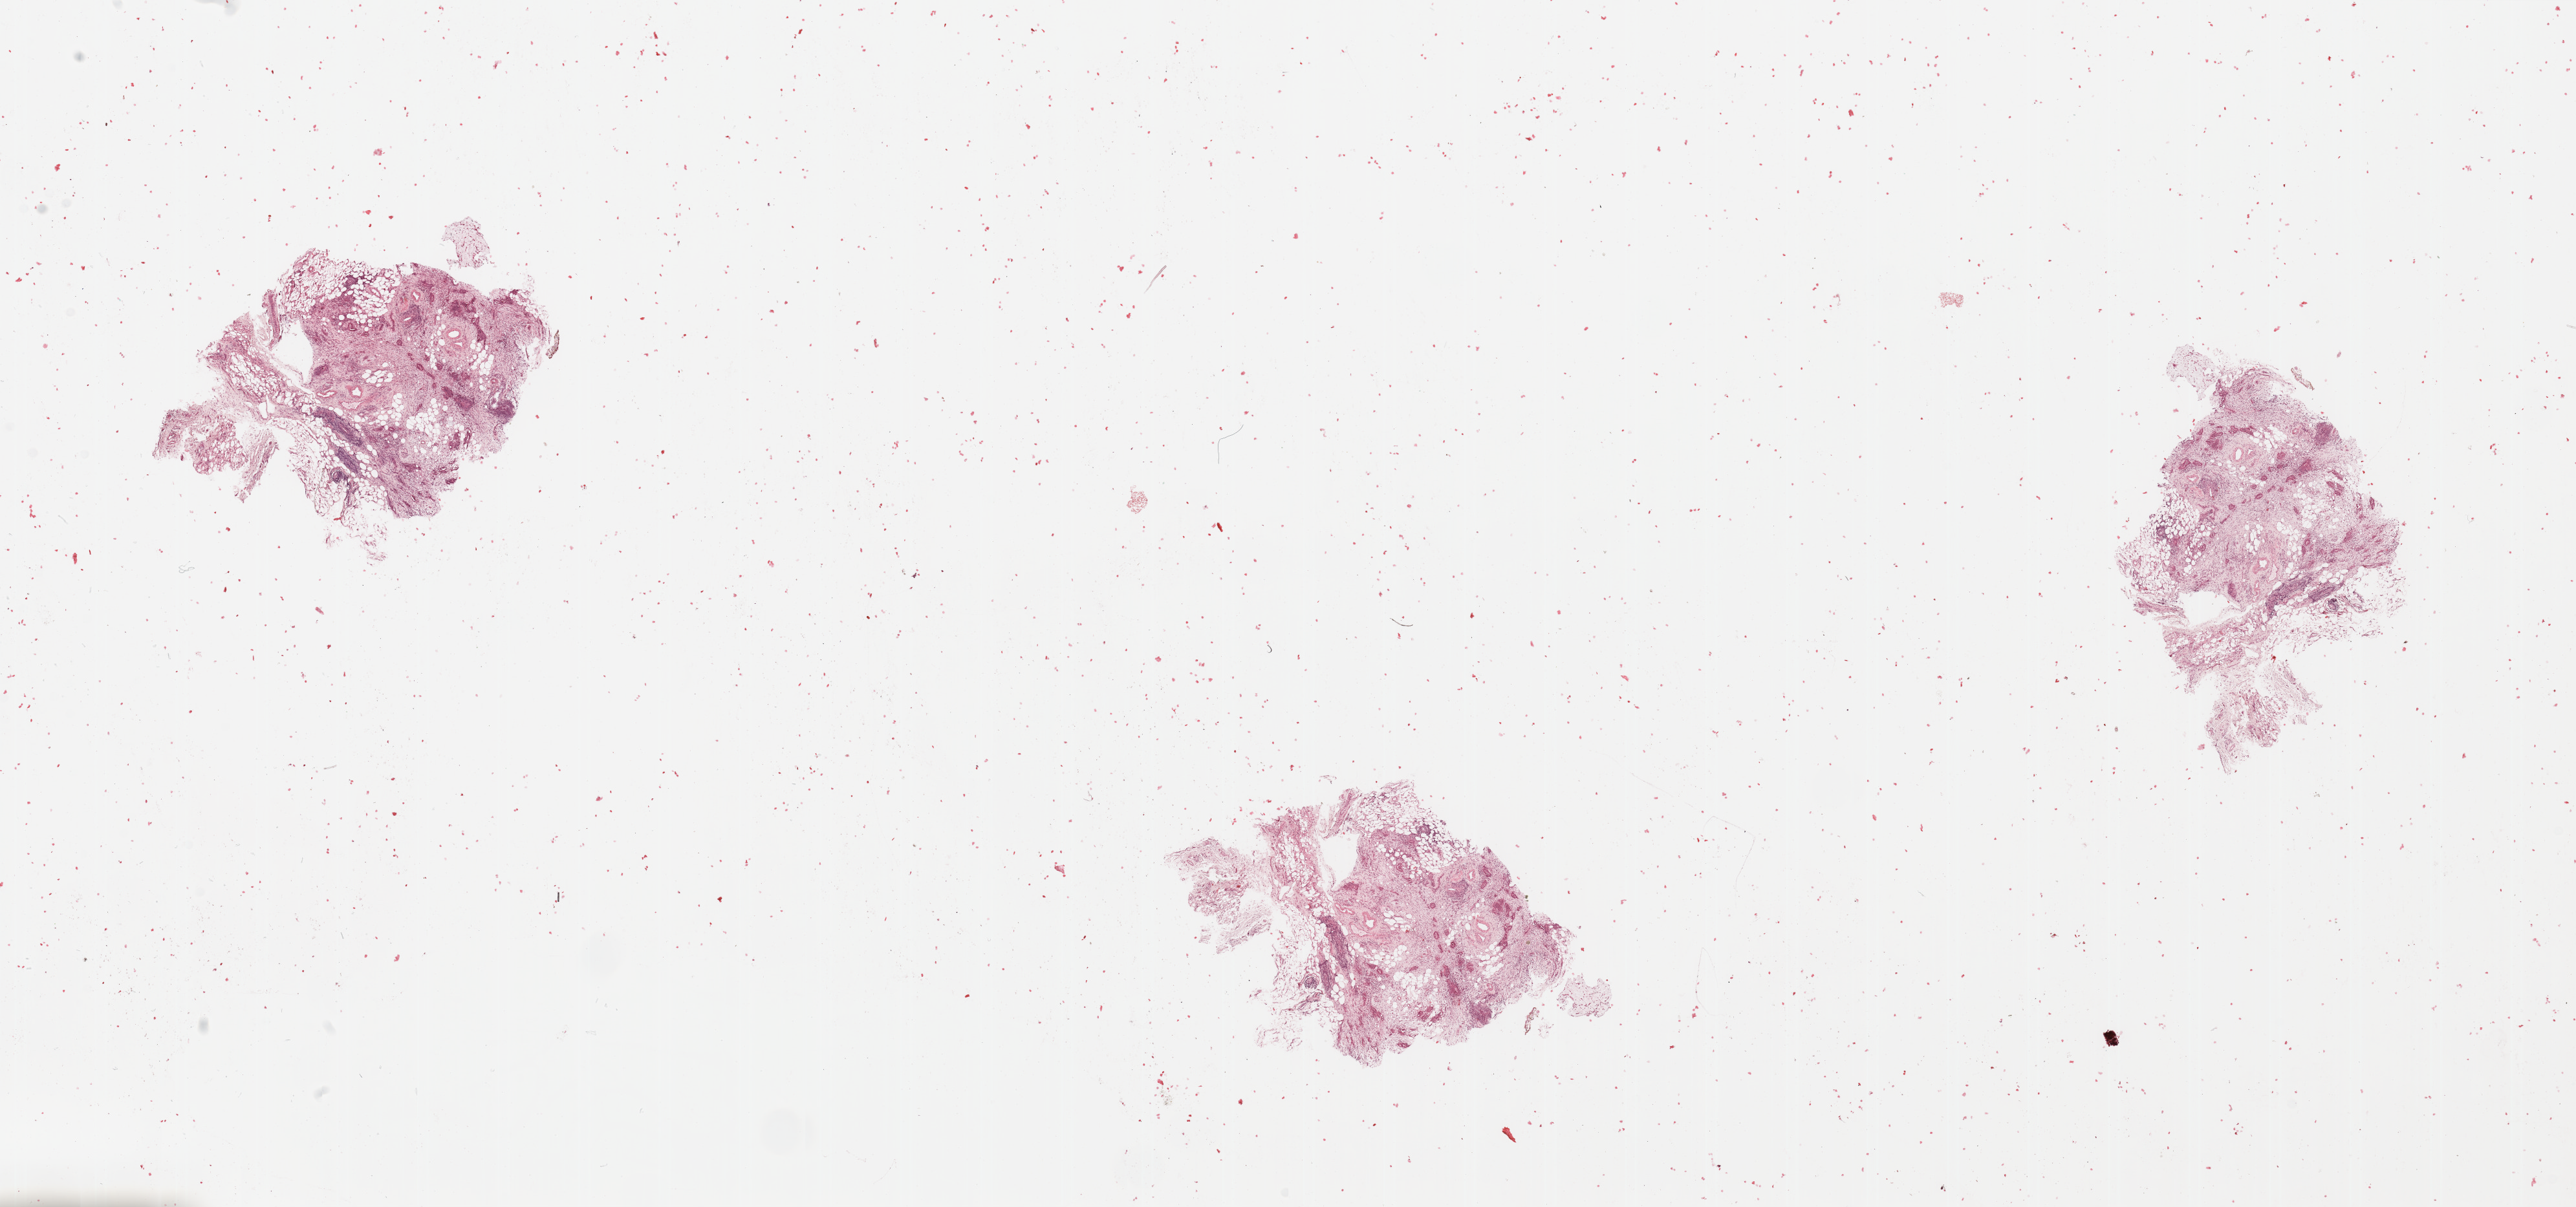
Digitized H&E-stained tissue section (whole slide), a low-resolution overview of the entire scanned area, about 31.5 x 14.8 mm, tumour tissue sample, sampled site: pancreas. Female, 63 y/o. Histologic grade: G2 (moderately differentiated). Slide review estimates, as recorded: tumour nuclei 10%, necrosis 0%.
AJCC pathologic stage: III. Primary tumour site (as recorded): head. Histologic diagnosis: Infiltrating duct carcinoma, NOS.